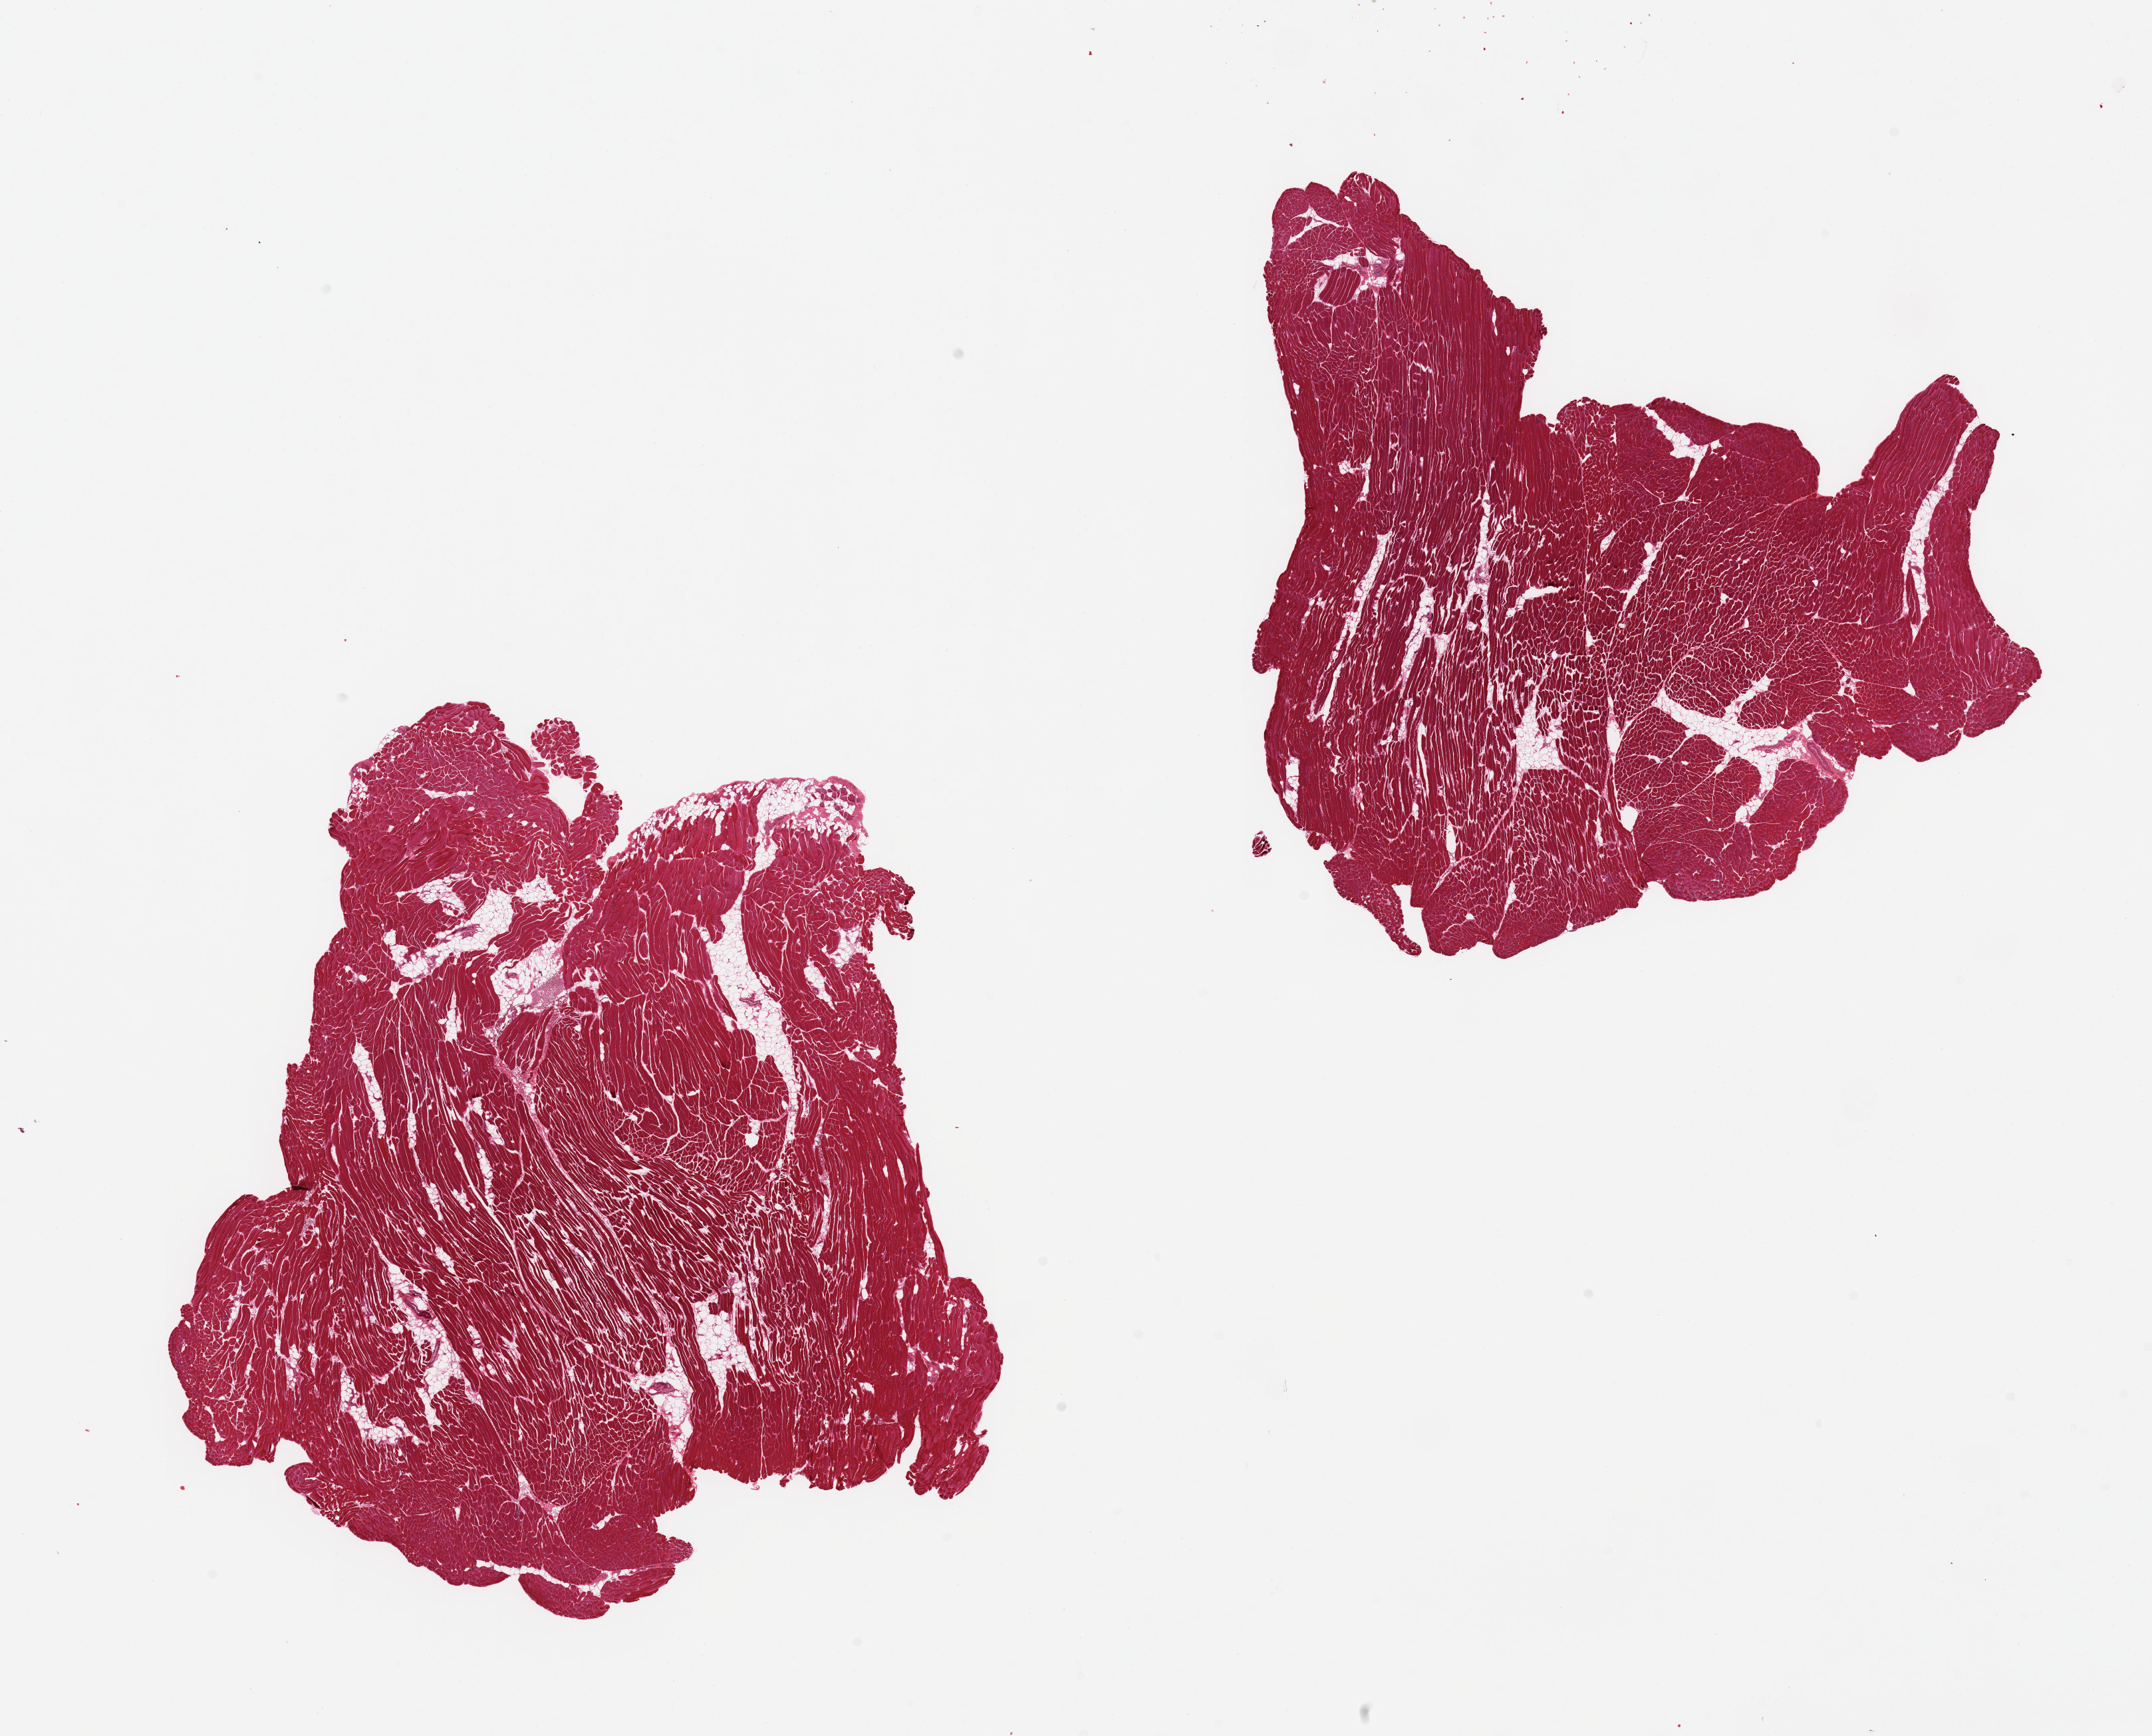
Digitized haematoxylin and eosin-stained section, brightfield — low-resolution overview of the scanned area, about 25.6 x 20.6 mm. PAXgene-fixed, paraffin-embedded tissue. Target tissue: skeletal muscle. Tissue donor sample.
Pathologist's review note for this sample: 2 pieces, 5-10% interstitial fat.